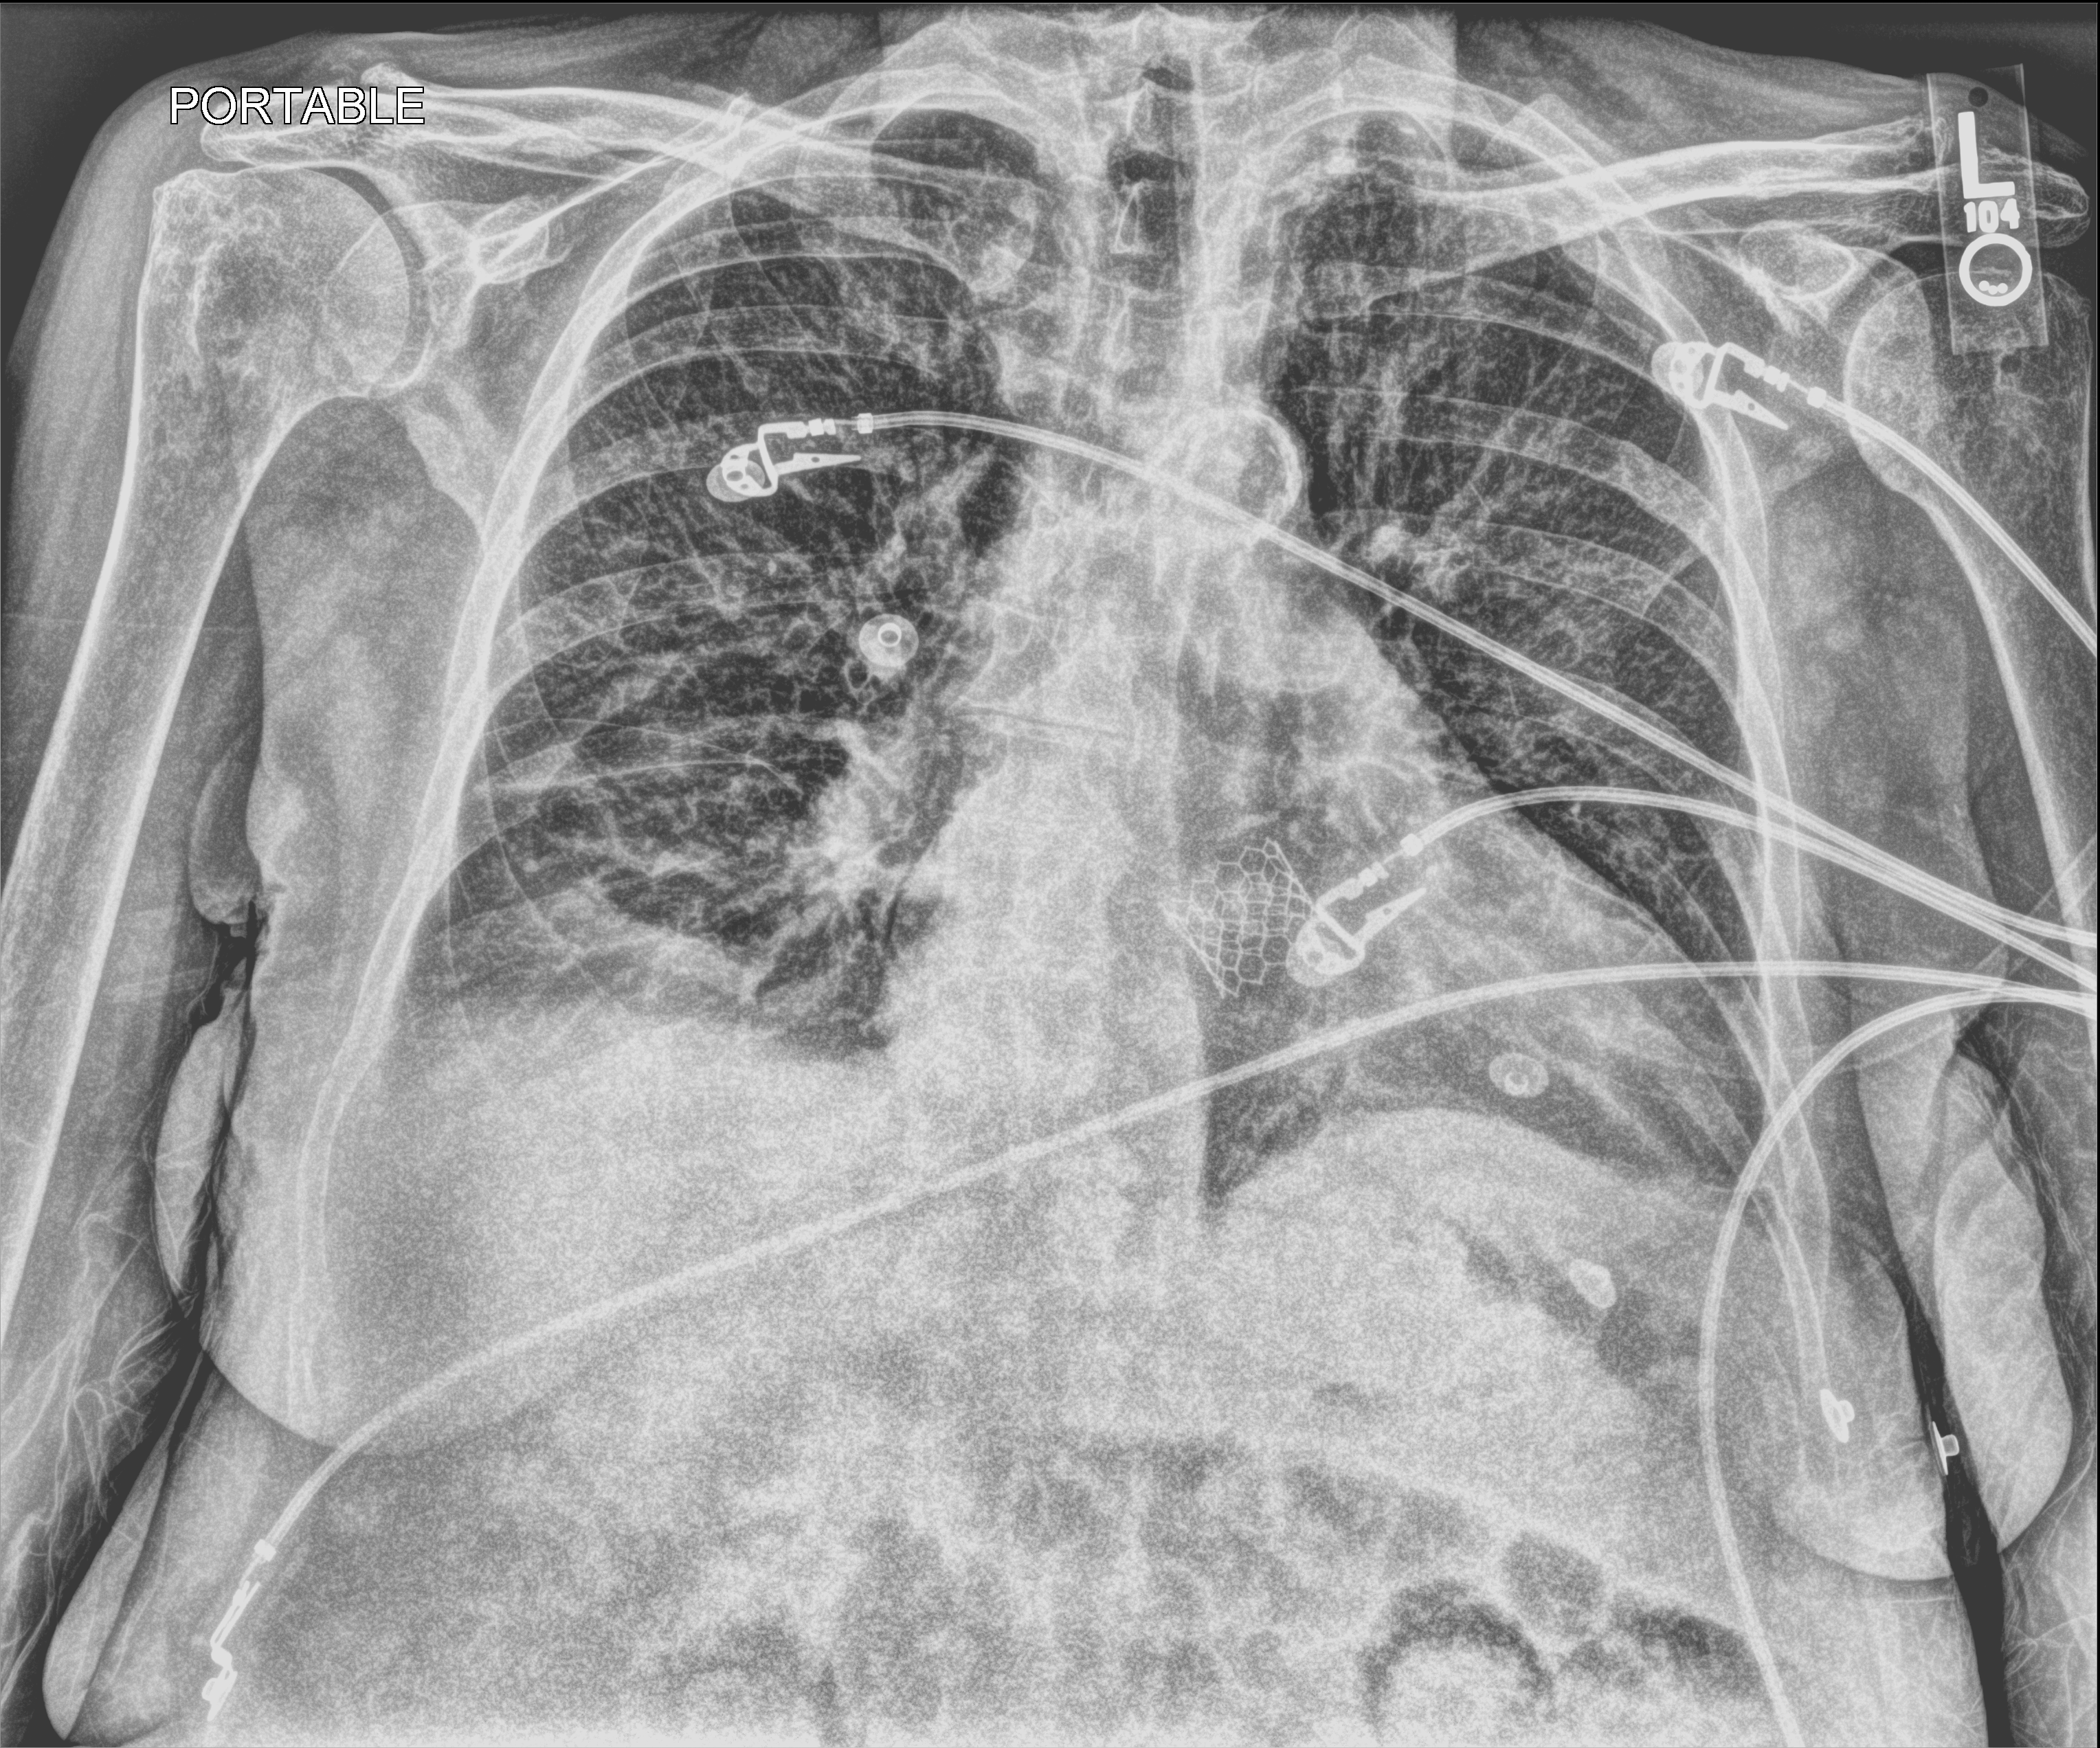
Portable chest radiograph; anteroposterior (AP) projection. Patient hospitalised with COVID-19; female, aged 75–90 years.
Admission-level facts for this patient (not findings on this image; timing relative to this image not recorded): admitted to intensive care during this hospital stay: no.